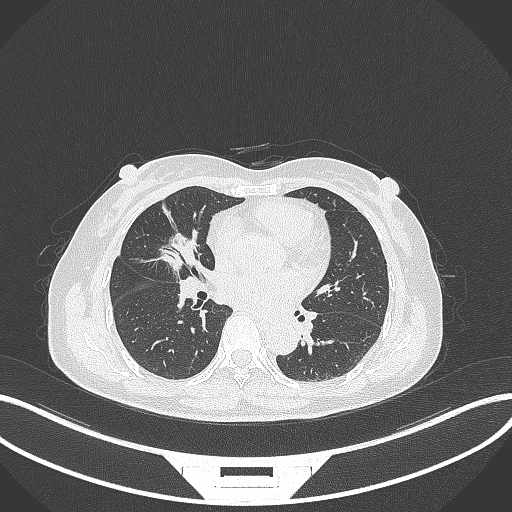
Chest CT, one axial slice. Position 145 of 284 along the scan axis. 120 kVp. Lung window (W 1500 / L -600 HU). 1 mm slice thickness. 512 × 512 image matrix, field of view 400 × 400 mm. Female patient, age 51 years. Case-level facts recorded for this patient, not image findings: clinical TNM (as recorded): T1c N0 M0; histopathological grade: G2.
Annotated regions visible in this slice (rectangle marked by the reading radiologist):
- lung tumour (recorded histology: adenocarcinoma): bounding box <158,232,201,274> (left, top, right, bottom; pixels)